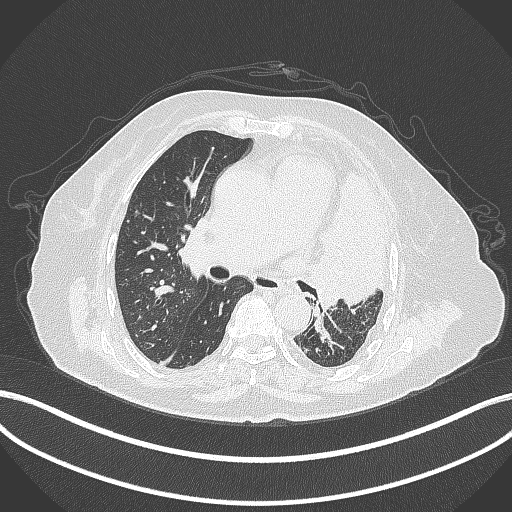
Chest CT, one axial slice. Position 217 of 399 along the scan axis. Lung window (W 1500 / L -600 HU). 1 mm slice thickness. 512 × 512 image matrix, field of view 400 × 400 mm. Patient: female, 75 years. From the clinical record (not read from this slice): clinical TNM (as recorded): T3 N3 M1.
Annotated regions visible in this slice (bounding box drawn by a radiologist):
- lung tumour (recorded histology: adenocarcinoma): bounding box <305,165,390,309> (left, top, right, bottom; pixels)